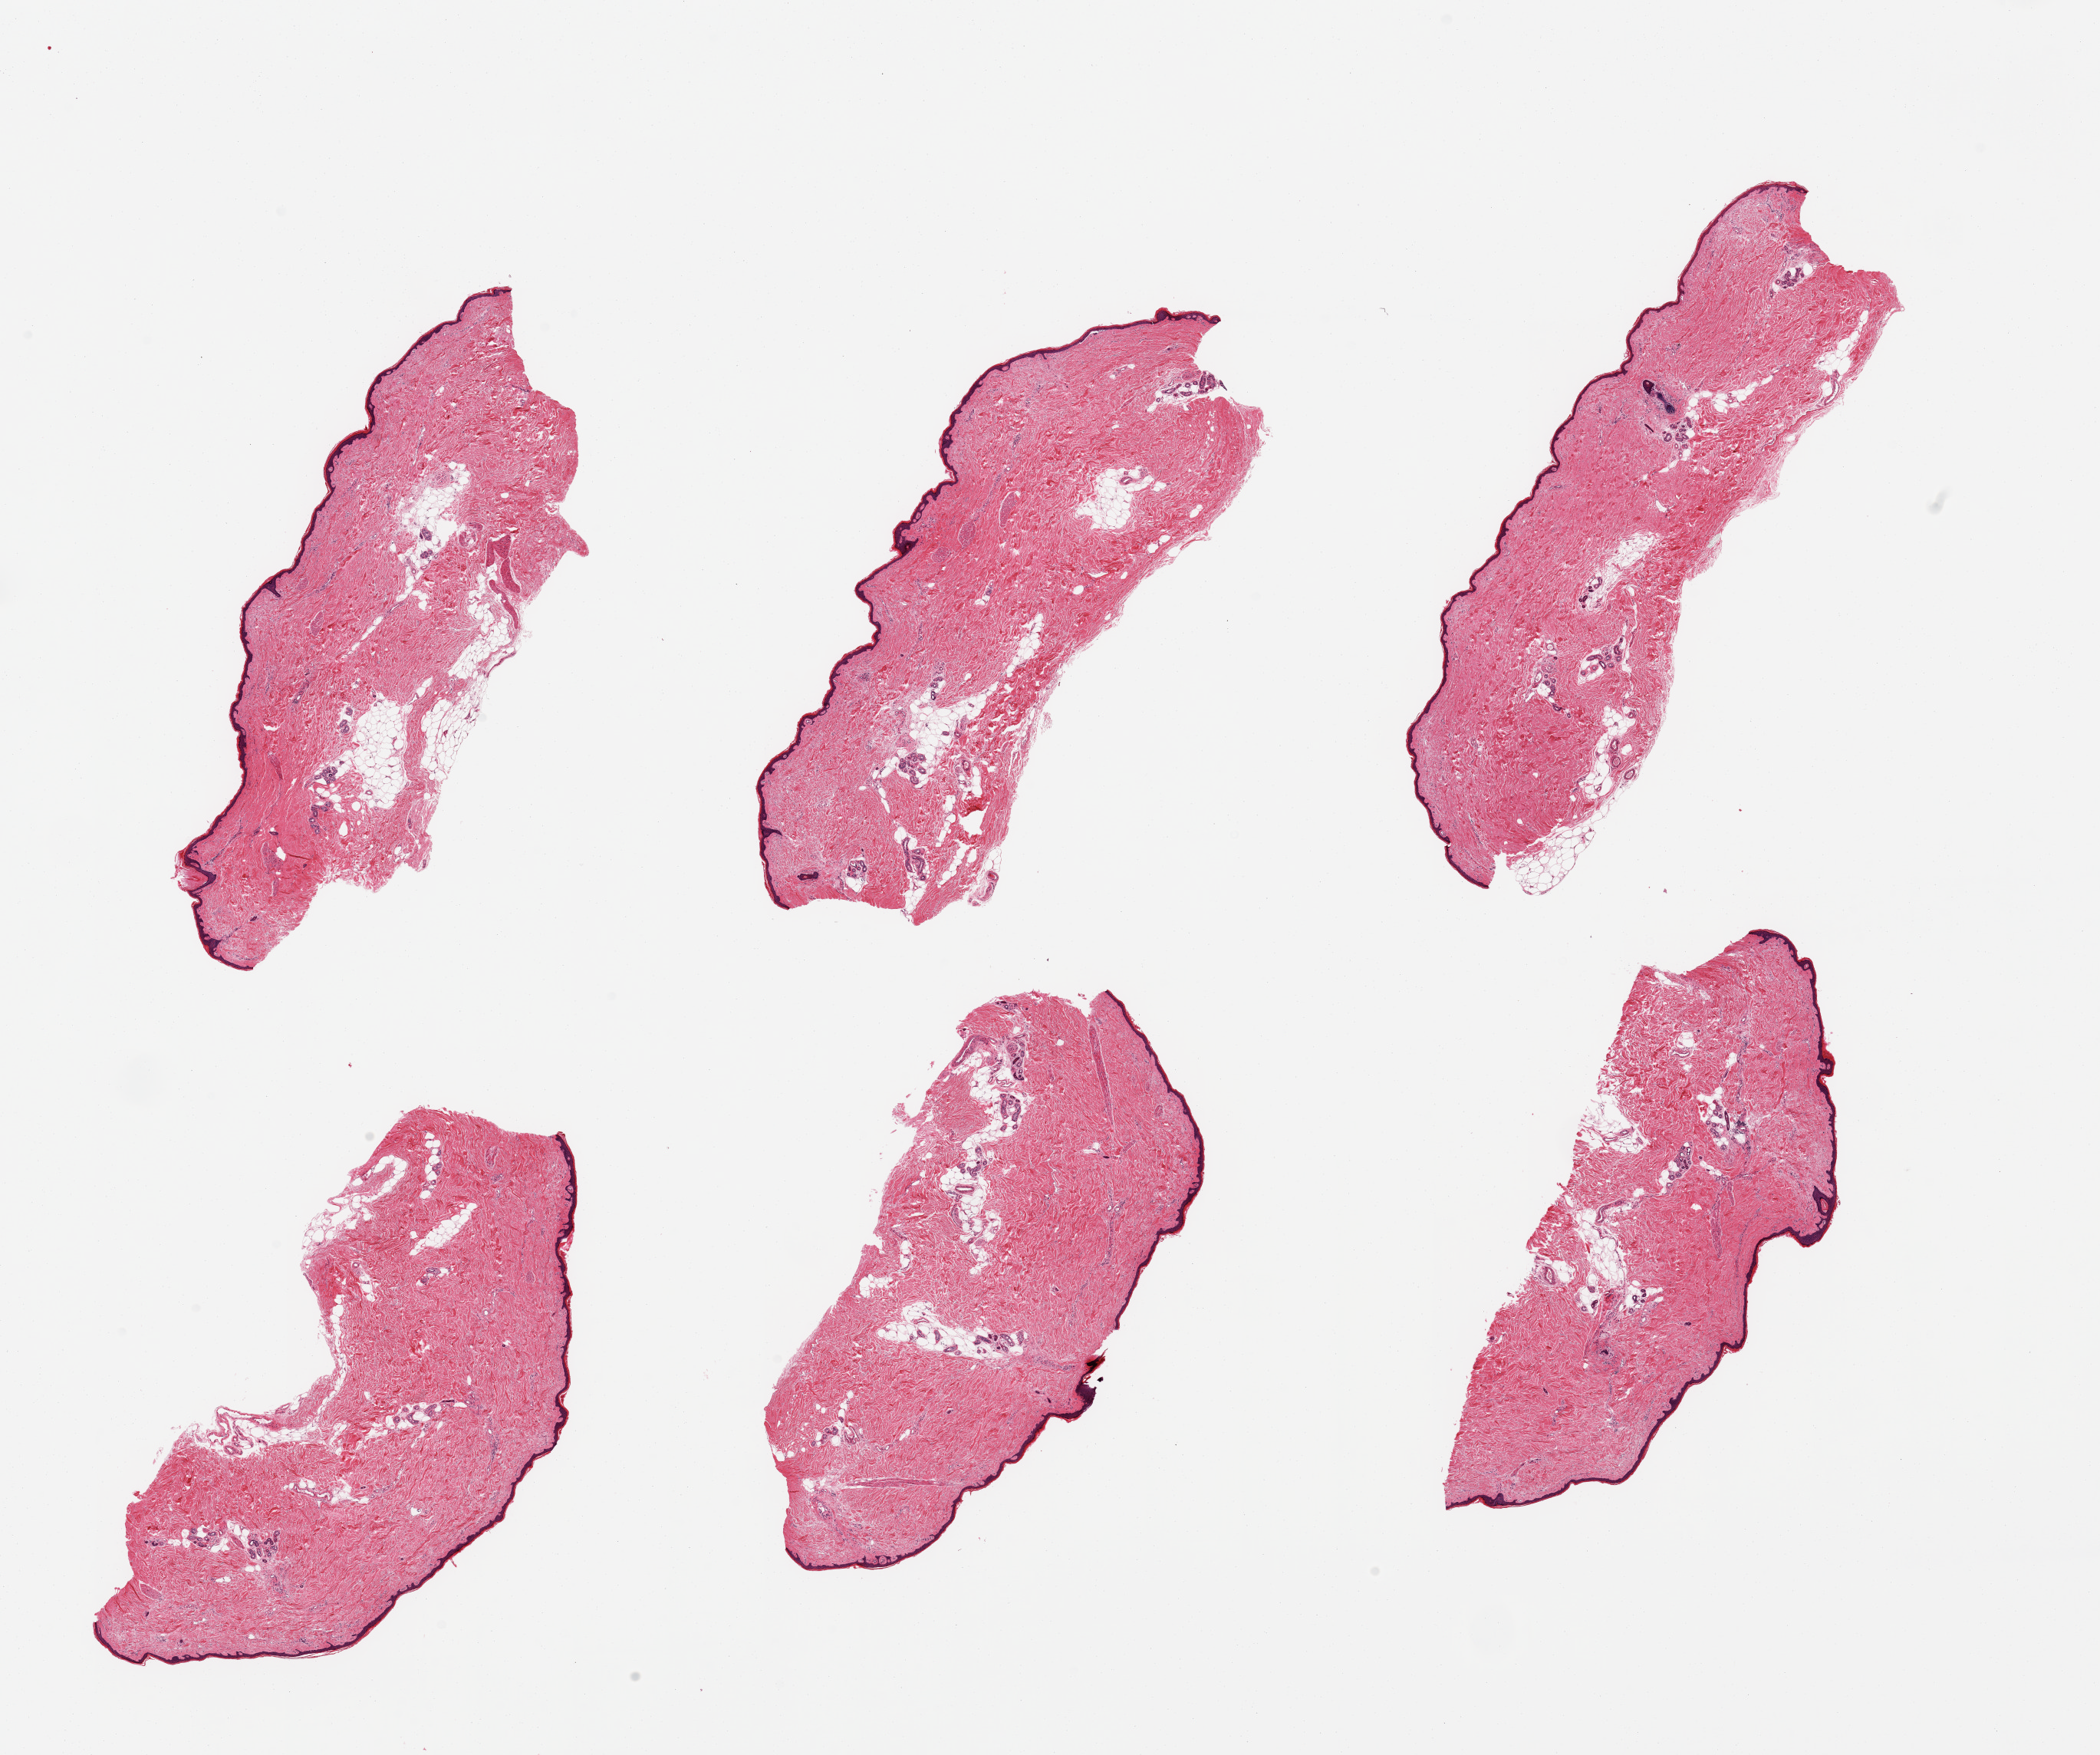
Whole-slide image, haematoxylin and eosin stain, brightfield — whole scanned area (about 21.7 x 18.1 mm) shown as a low-resolution overview, PAXgene-fixed, paraffin-embedded tissue, target tissue: skin of lower leg, tissue donor sample. Donor sex: female.
• pathologist's review note for this sample: 6 pieces; 10 to 20% internal (periadnexal) fat; epidermis is ~35 microns